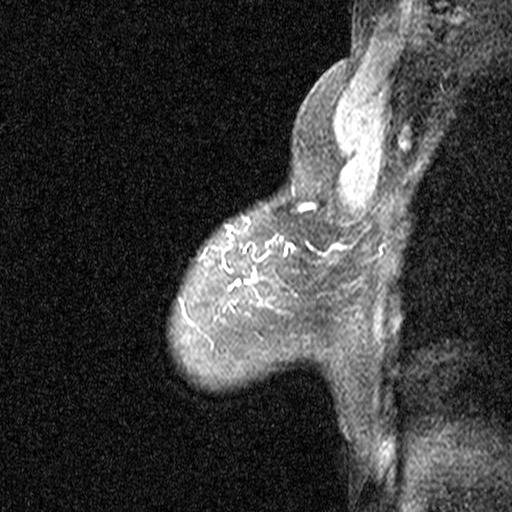
Breast MRI (dynamic contrast-enhanced), one sagittal slice. Position 35 of 44 along the scan axis. Dynamic contrast-enhanced study with each time point stored as its own series, time point 2 of 3 at this slice position (early post-contrast, ordered by acquisition time). 1.5 T. TE 4.5 ms, TR 11 ms. 512 × 512 image matrix. Patient: female, 53 years. Case-level facts recorded for this patient, not image findings: setting: breast cancer imaged before/during neoadjuvant chemotherapy; receptor status: HR-positive, HER2-negative.
Outlined on this slice (semi-automatic segmentation, software-assisted and operator-edited):
- analysis volume of interest (the breast-tissue region the enhancement analysis was run in; not a lesion): box from (x=88, y=176) to (x=313, y=423) px
- tumour enhancement mask (voxels above the 90 % enhancement threshold inside the analysis volume of interest): (x=253, y=204)–(x=308, y=277)